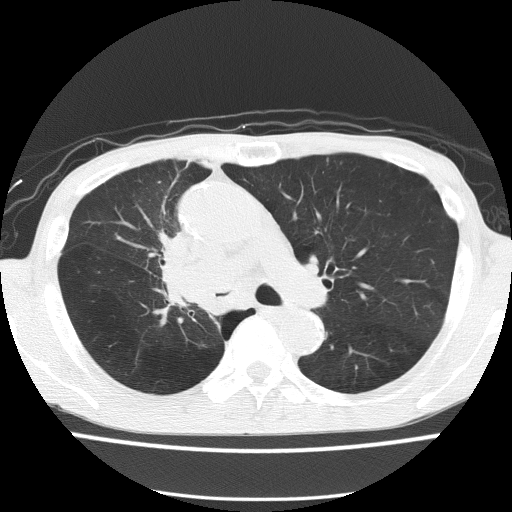
Axial slice from a low-dose chest CT screening exam. First (baseline) screen. Lung window (W 1500 / L -600 HU). 2 mm slice thickness. Slice 56 of 150 in the series. Male participant, aged 59 years at enrolment. Former smoker at enrolment.
Expert-annotated lung lesion, bounding box (x1, y1, x2, y2) in pixels: (141, 230, 232, 321). The screening reader recorded 5 non-calcified nodules or masses ≥4 mm on this exam; which of them this box marks is not recorded. Later outcome: lung cancer diagnosed 72 days after this screen — squamous cell carcinoma, NOS, right upper lobe, moderately differentiated (G2), stage IV (AJCC 6th edition).